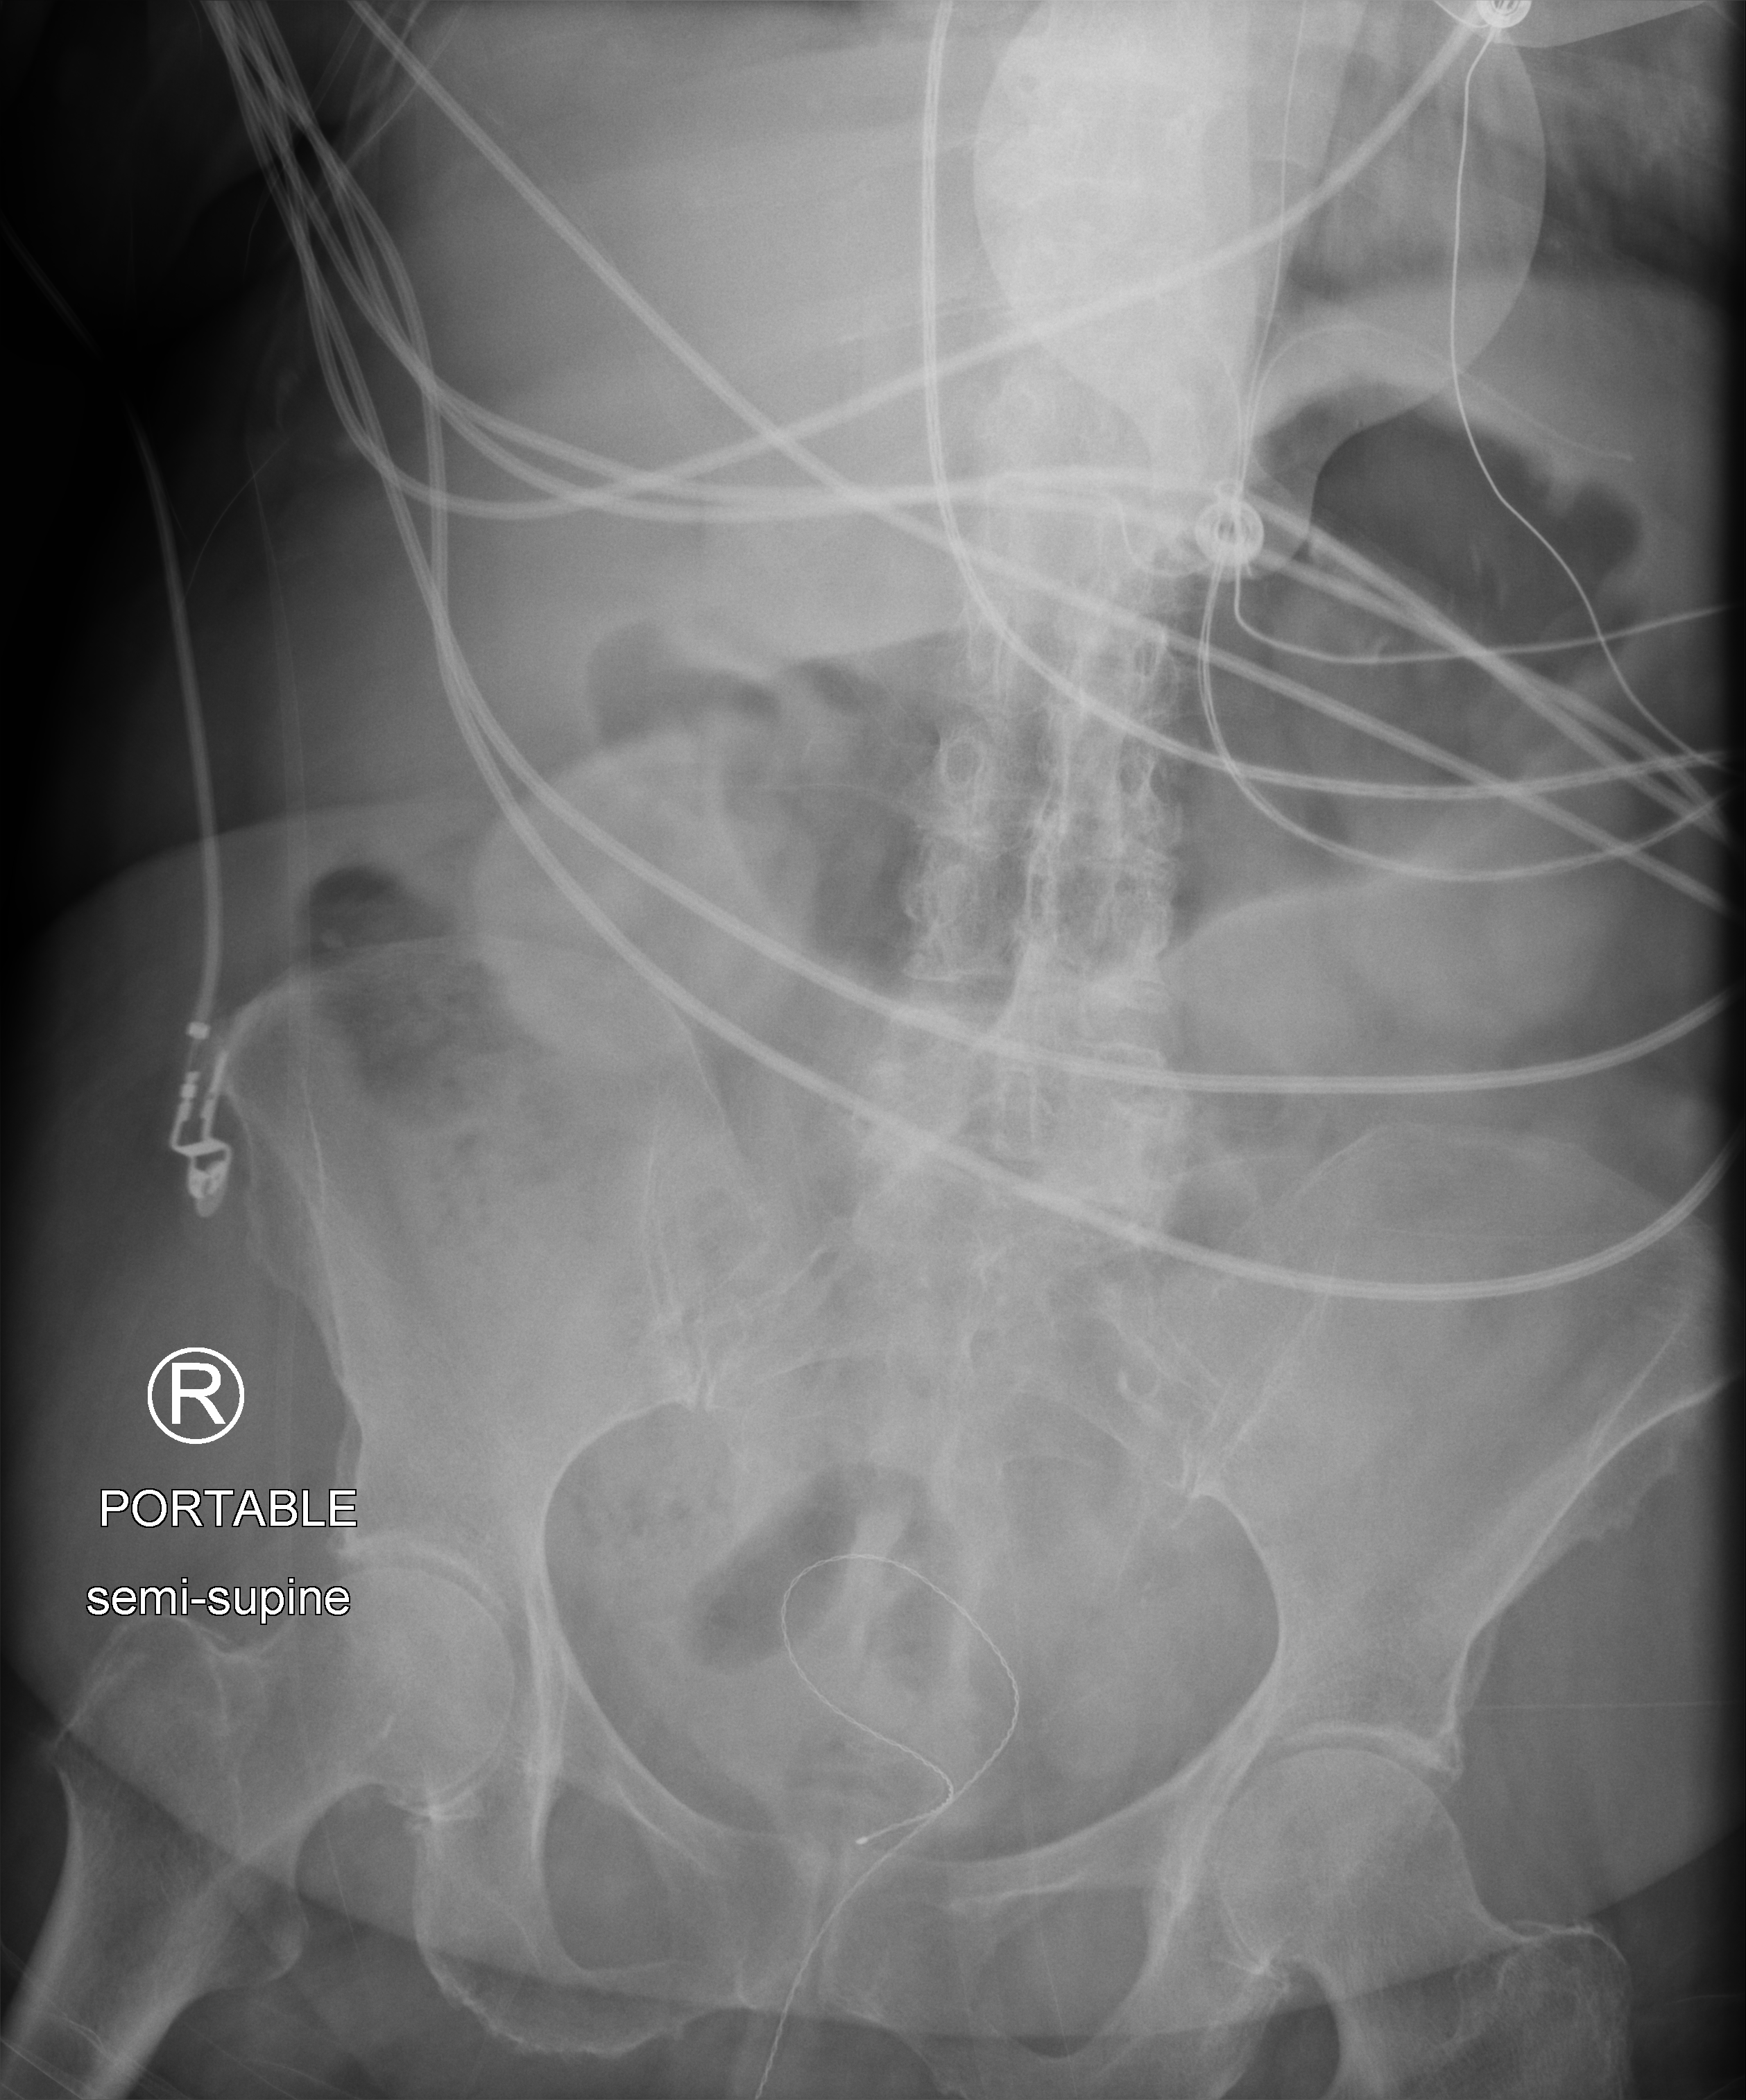
Abdomen X-ray (portable), anteroposterior (AP) projection. Patient hospitalised with COVID-19; female, aged 75–90 years.
Admission-level facts for this patient (not findings on this image; timing relative to this image not recorded):
- length of hospital stay: 2 days
- admitted to intensive care during this hospital stay: yes